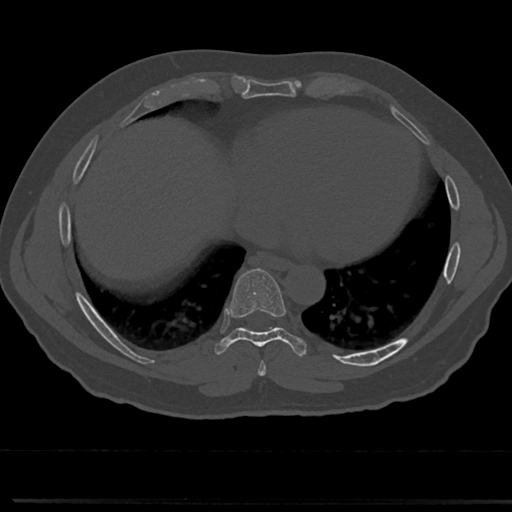
CT including the spine, one axial slice; slice 353 of 817 in the series (ordered by position); reconstruction kernel Br40s/3; 120 kVp; bone window (W 1800 / L 400 HU); 512 × 512 image matrix, field of view 355 × 355 mm. Patient: male, 61 years. Case-level facts recorded for this patient, not image findings: primary cancer: prostate.
Structures marked on this image (semi-automatically segmented with operator editing):
- T7 vertebra: bounding box <244,331,282,375> (left, top, right, bottom; pixels)
- T8 vertebra: <223,270,285,345>